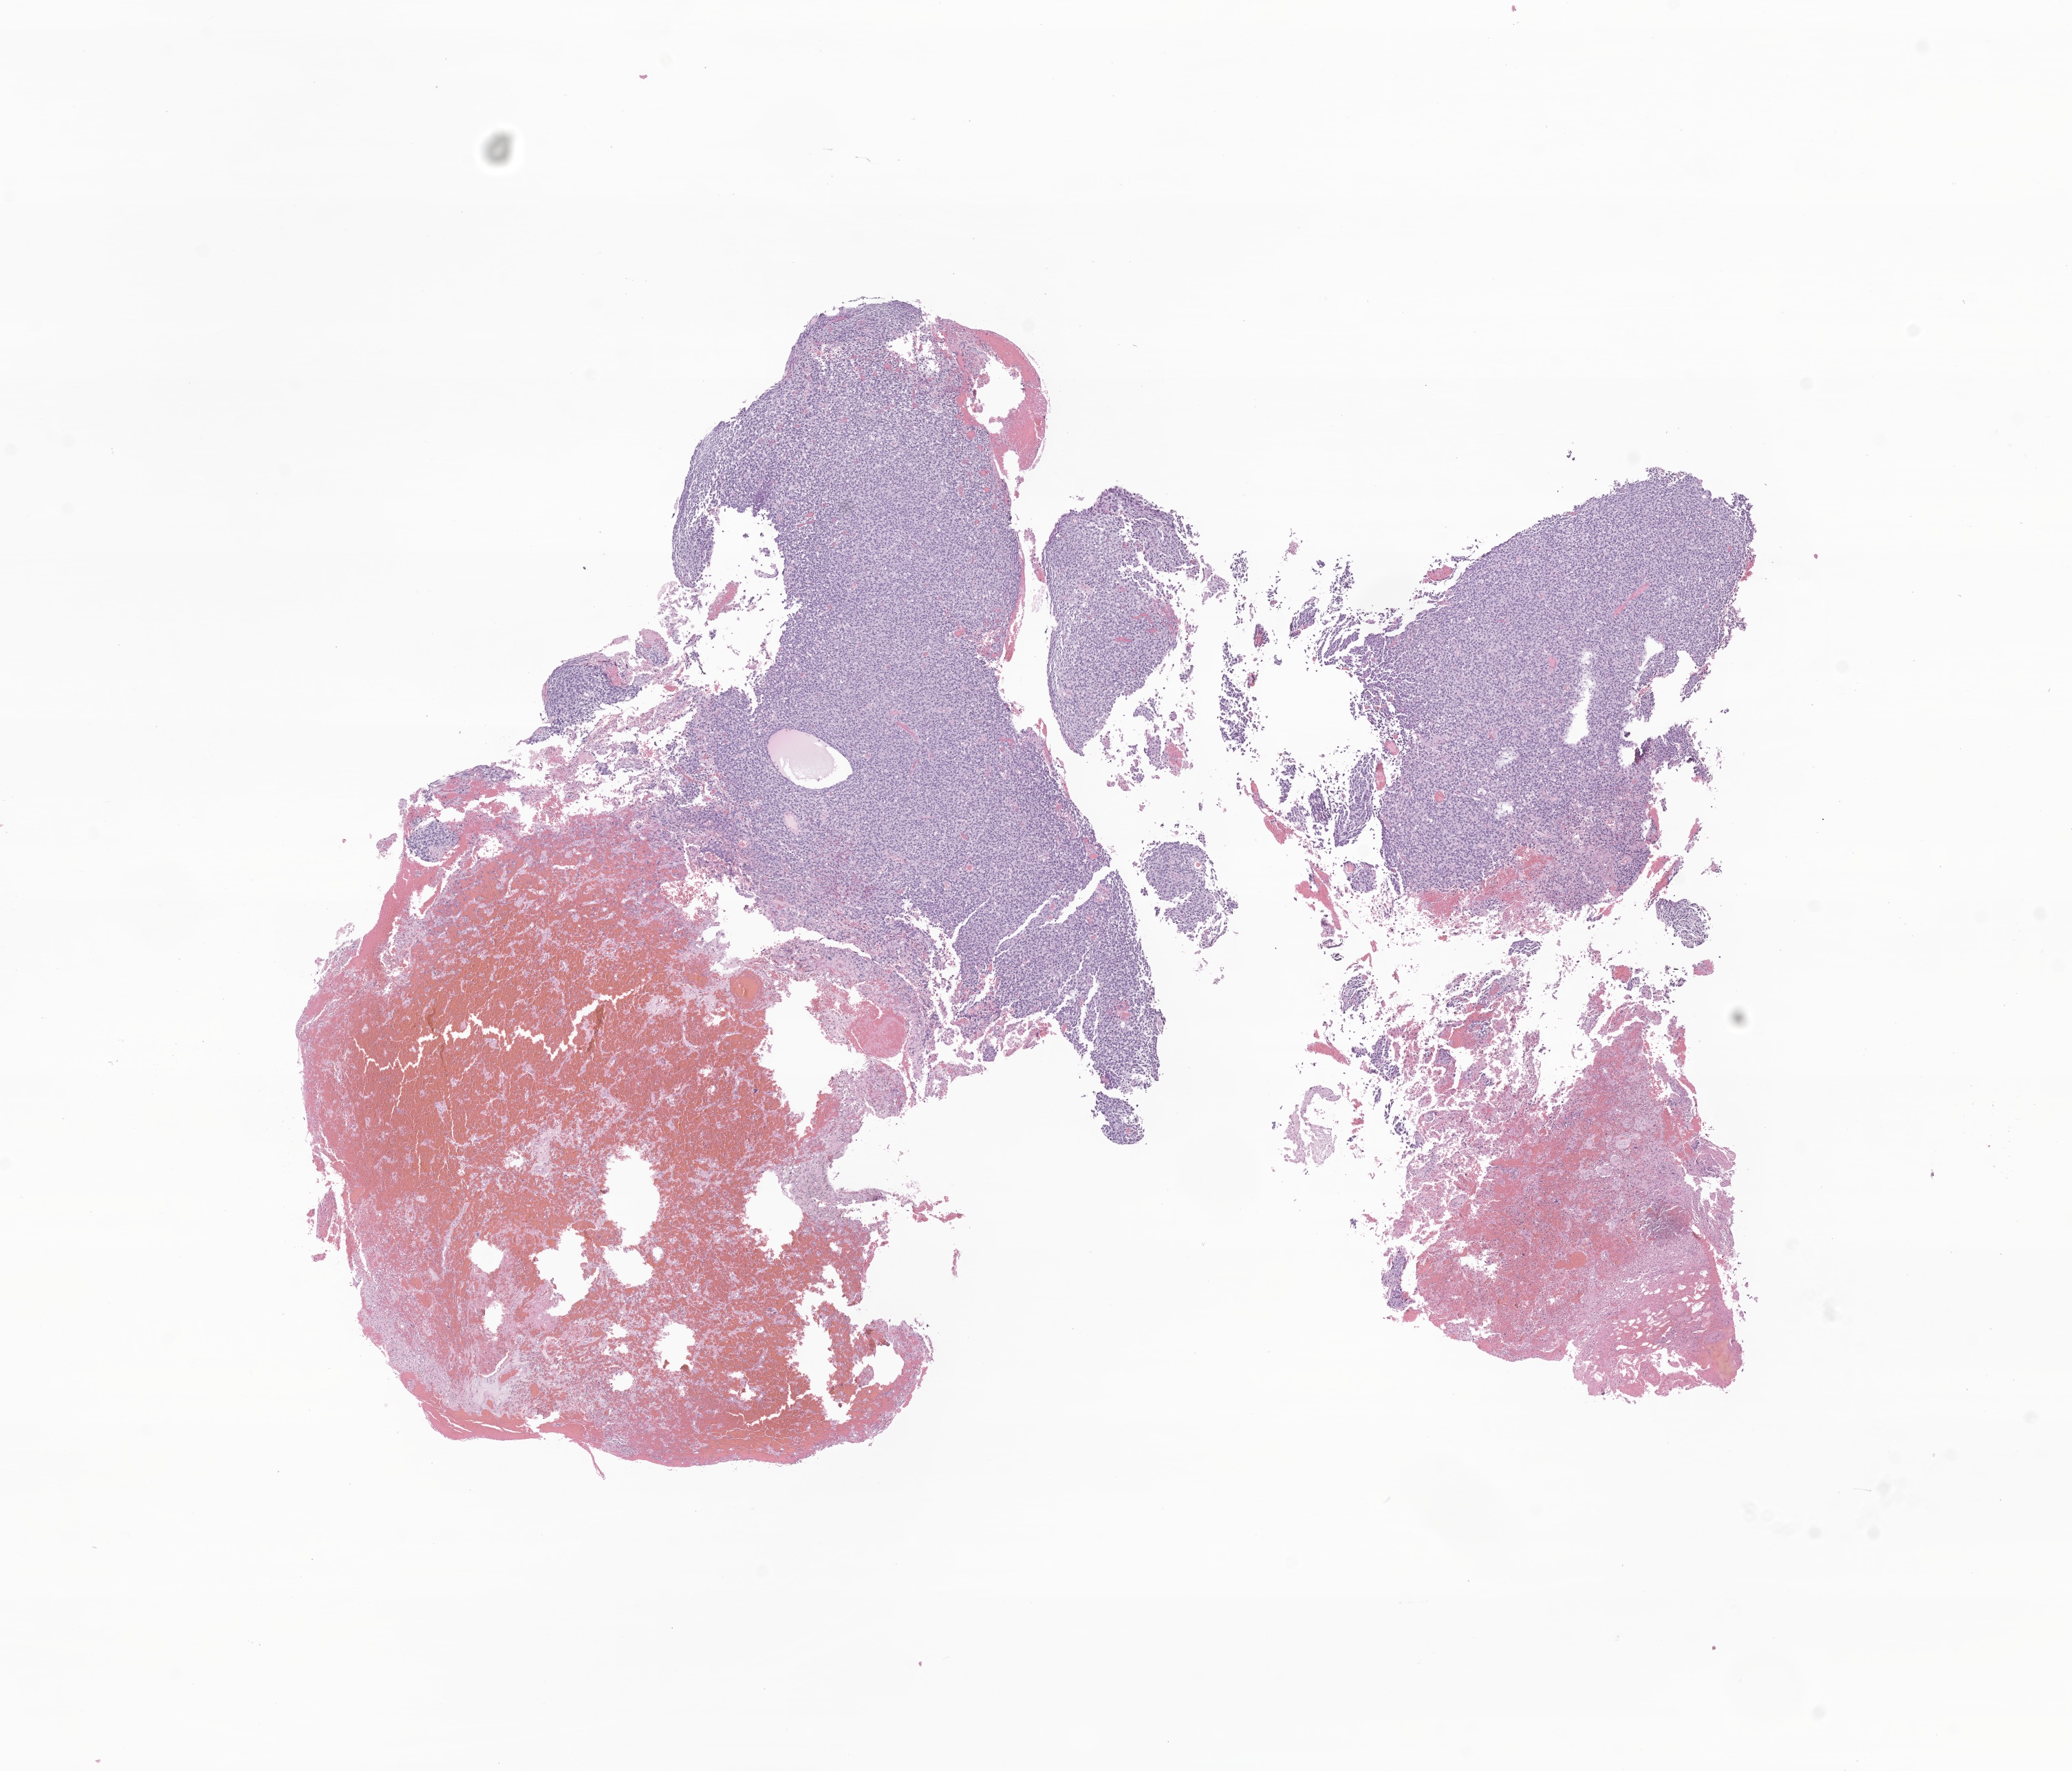
Digitized H&E-stained section of tumor tissue from the pleura, low-resolution overview of the scanned area, about 12.7 x 10.9 mm; formalin-fixed, paraffin-embedded (FFPE) tissue. Patient male; age 57 months (4 years 9 months).
Recorded diagnosis: Pleuropulmonary blastoma.